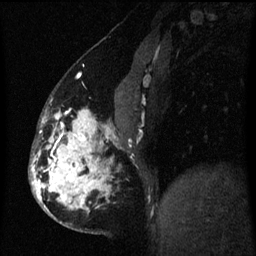
Breast MRI (dynamic contrast-enhanced), one sagittal slice. Slice 24 of 60 in the series (ordered by position). Dynamic contrast-enhanced series, image 2 of 3 at this slice position (ordered by acquisition). 1.5 T. TE 4.2 ms, TR 8 ms. 256 × 256 image matrix, field of view 190 × 190 mm. Patient: female, 50 years.
Structures marked on this image (semi-automatic segmentation, software-assisted and operator-edited):
- analysis volume of interest (the breast-tissue region the enhancement analysis was run in; not a lesion): bounding box <32,104,117,233> (left, top, right, bottom; pixels)
- tumour enhancement mask (voxels above the 70 % enhancement threshold inside the analysis volume of interest): <32,110,110,209>